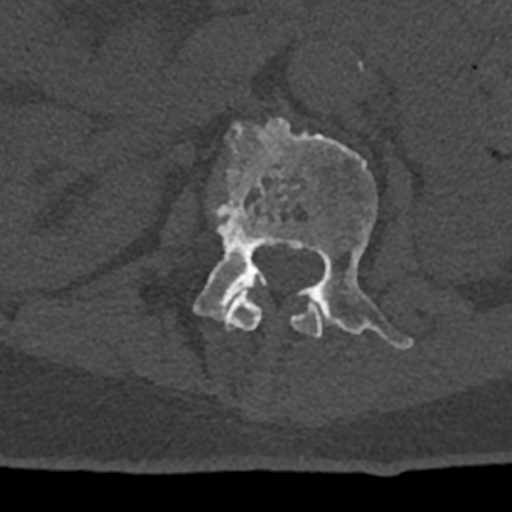
CT including the spine, one axial slice; slice 395 of 797 in the series (ordered by position); bone window (W 1800 / L 400 HU); 0.5 mm slice thickness; 512 × 512 image matrix, field of view 160 × 160 mm. Male patient, age 74 years. From the clinical record (not read from this slice): primary cancer: renal.
Annotated regions visible in this slice (semi-automatic segmentation, software-assisted and operator-edited):
- L1 vertebra: bounding box <211,206,323,337> (left, top, right, bottom; pixels)
- L2 vertebra: <193,117,413,349>